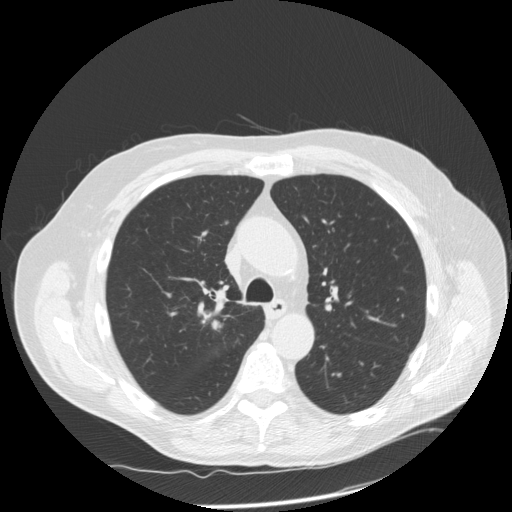
Low-dose screening chest CT, one axial slice; slice 112 of 166 in the series (ordered by position); reconstruction kernel STANDARD; 120 kVp; lung window (W 1500 / L -600 HU); 2.5 mm slice thickness; 512 × 512 image matrix, field of view 390 × 390 mm.
Annotated regions visible in this slice (expert manual segmentation):
- lesion 1 (tumor, upper lobe of right lung): bounding box <213,322,218,328> (left, top, right, bottom; pixels)